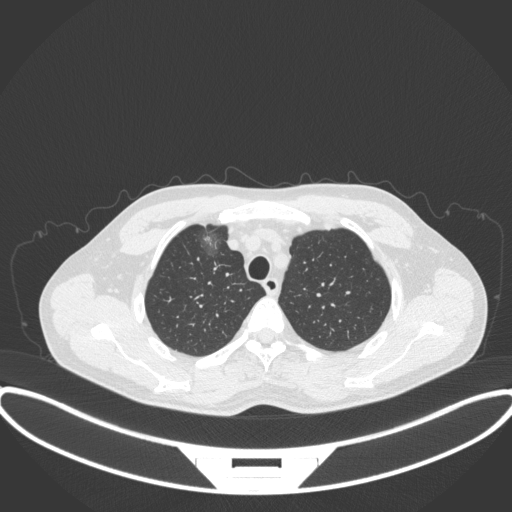
Chest CT, one axial slice. Position 298 of 395 along the scan axis. Reconstruction kernel B31f. Lung window (W 1500 / L -600 HU). 1 mm slice thickness. 512 × 512 image matrix, field of view 424 × 424 mm. Male patient, age 60 years. From the clinical record (not read from this slice): clinical TNM (as recorded): T1c N0 M0.
Annotated regions visible in this slice (bounding box drawn by a radiologist):
- lung tumour (recorded histology: adenocarcinoma): bounding box (x1, y1, x2, y2) in pixels: (200, 228, 224, 261)